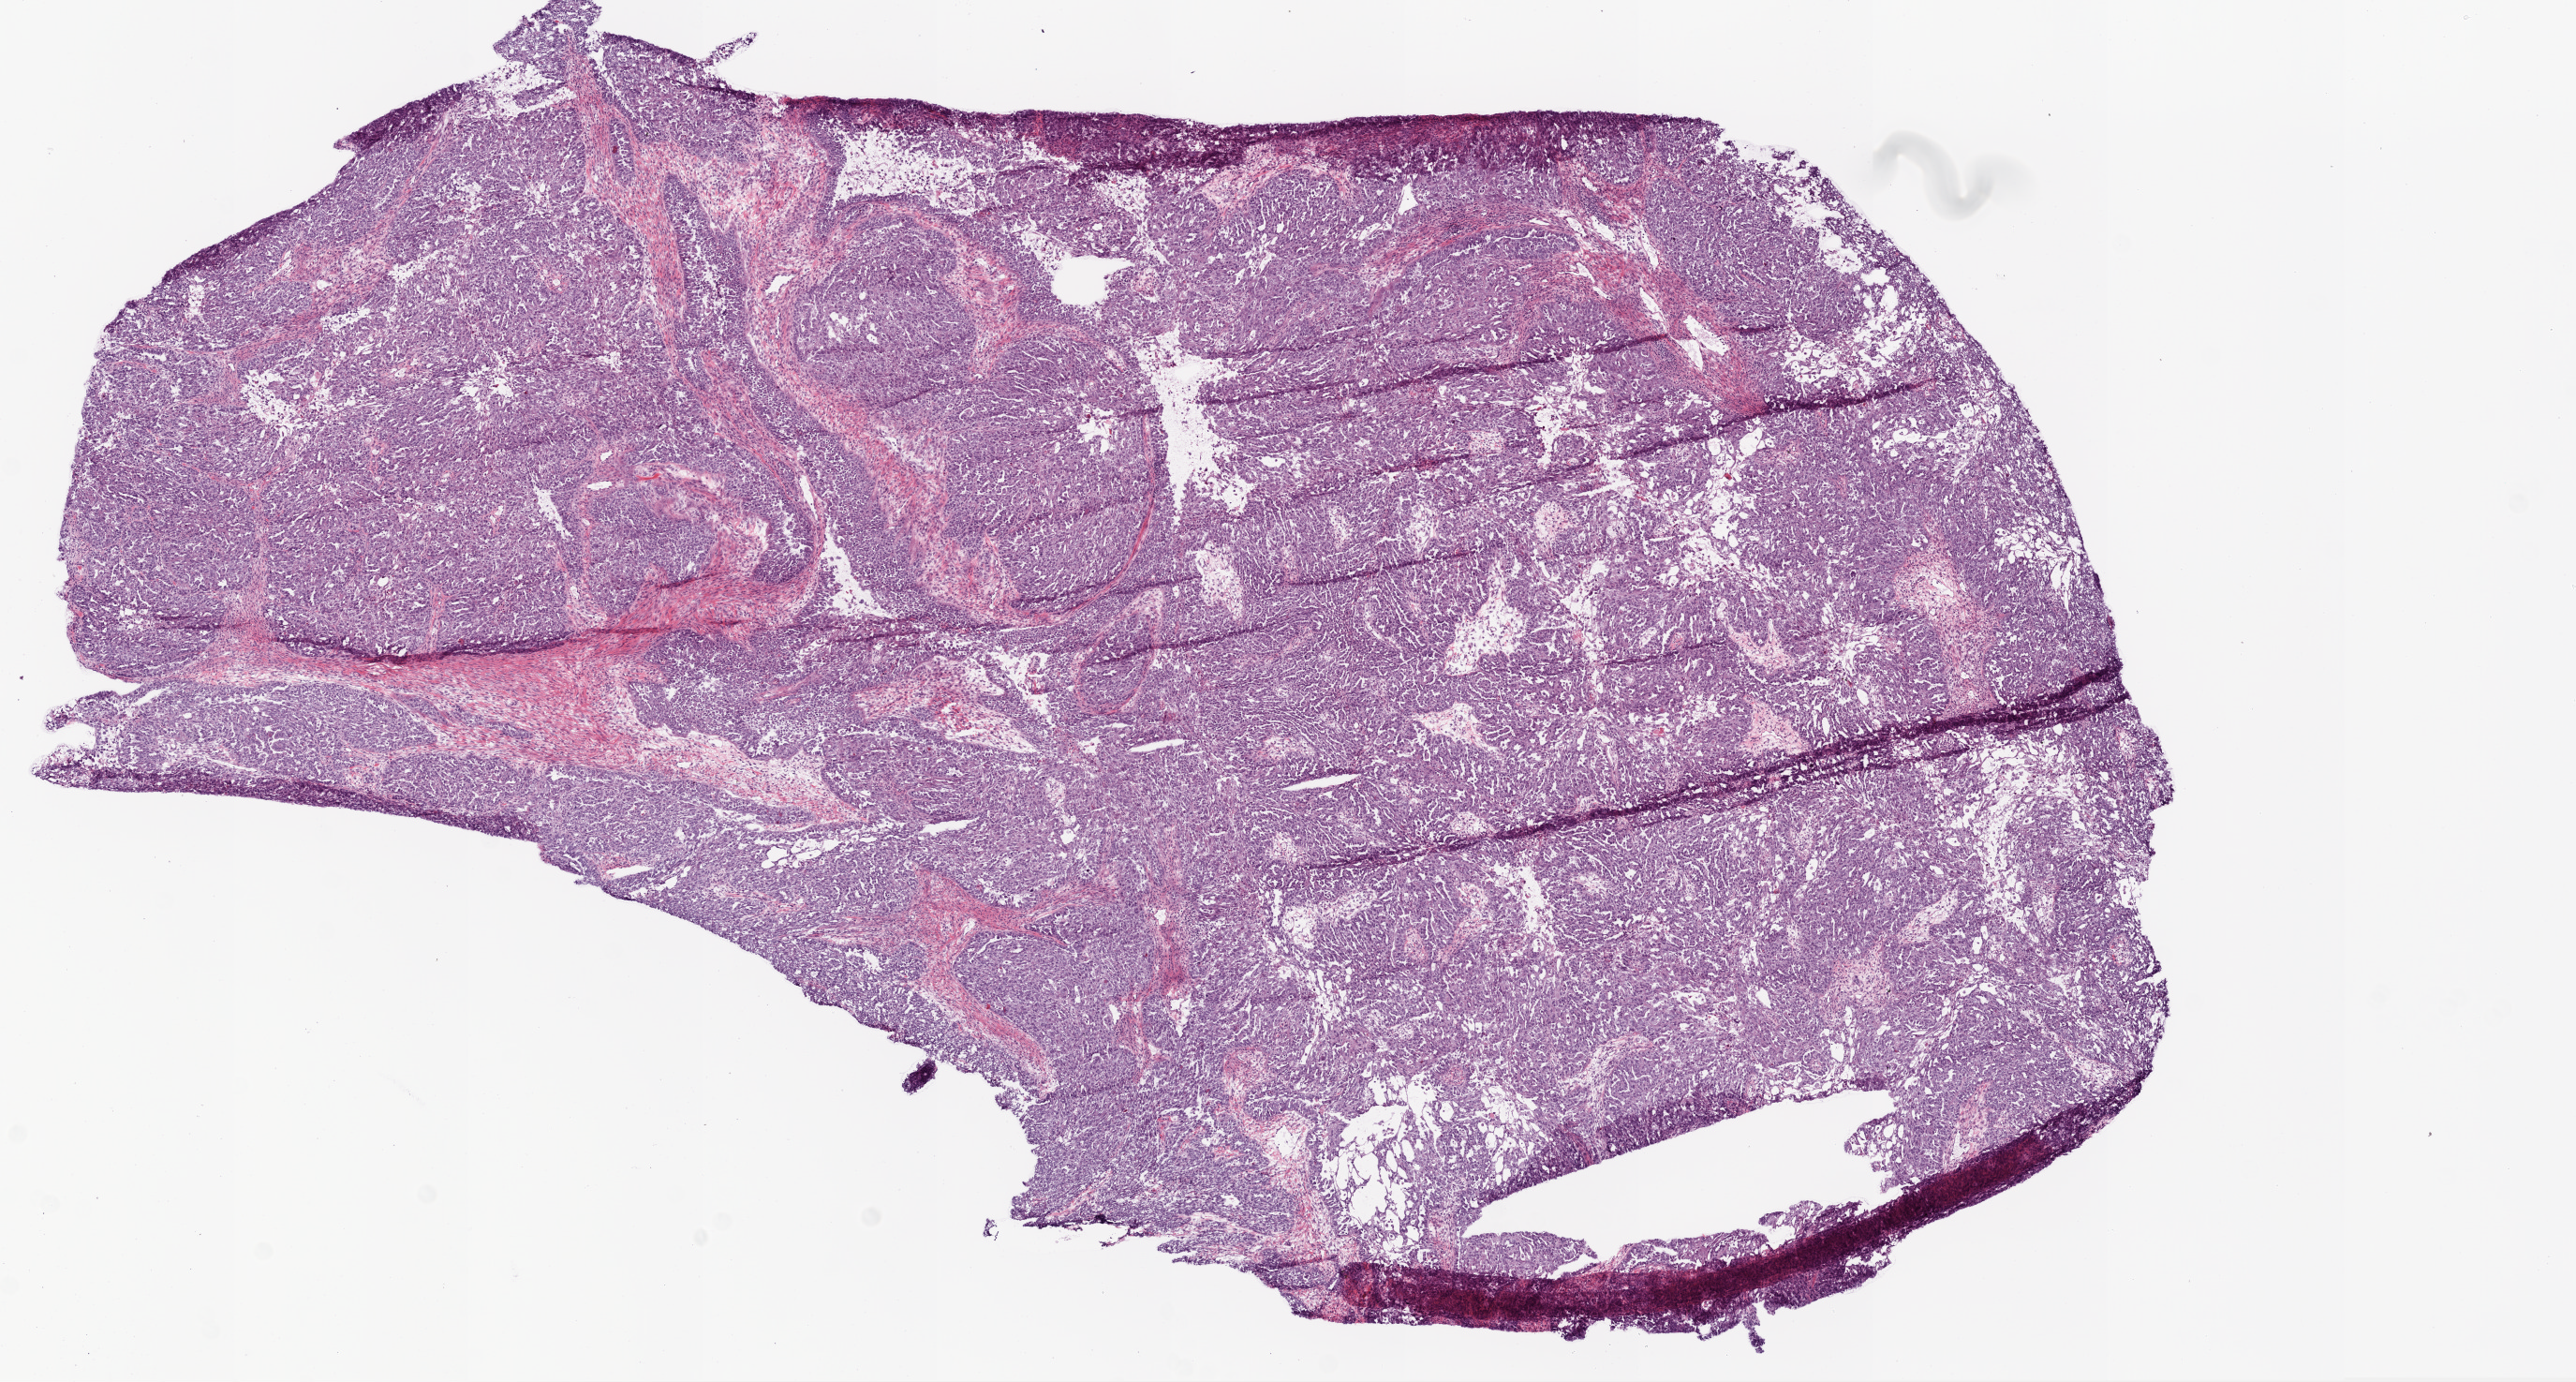
H&E-stained whole-slide image — shown as a low-resolution overview of the whole scanned area (about 11.0 x 5.9 mm); frozen section; sample: primary tumour, ovary. Female, age 53 years at initial diagnosis. Histologic grade: G3 (poorly differentiated). Composition of this section per pathologist review: tumour cells 95%, tumour nuclei 95%, normal cells 0%, stromal cells 5%, necrosis 0%.
* FIGO stage: IIIB
* diagnosis: Serous cystadenocarcinoma, NOS